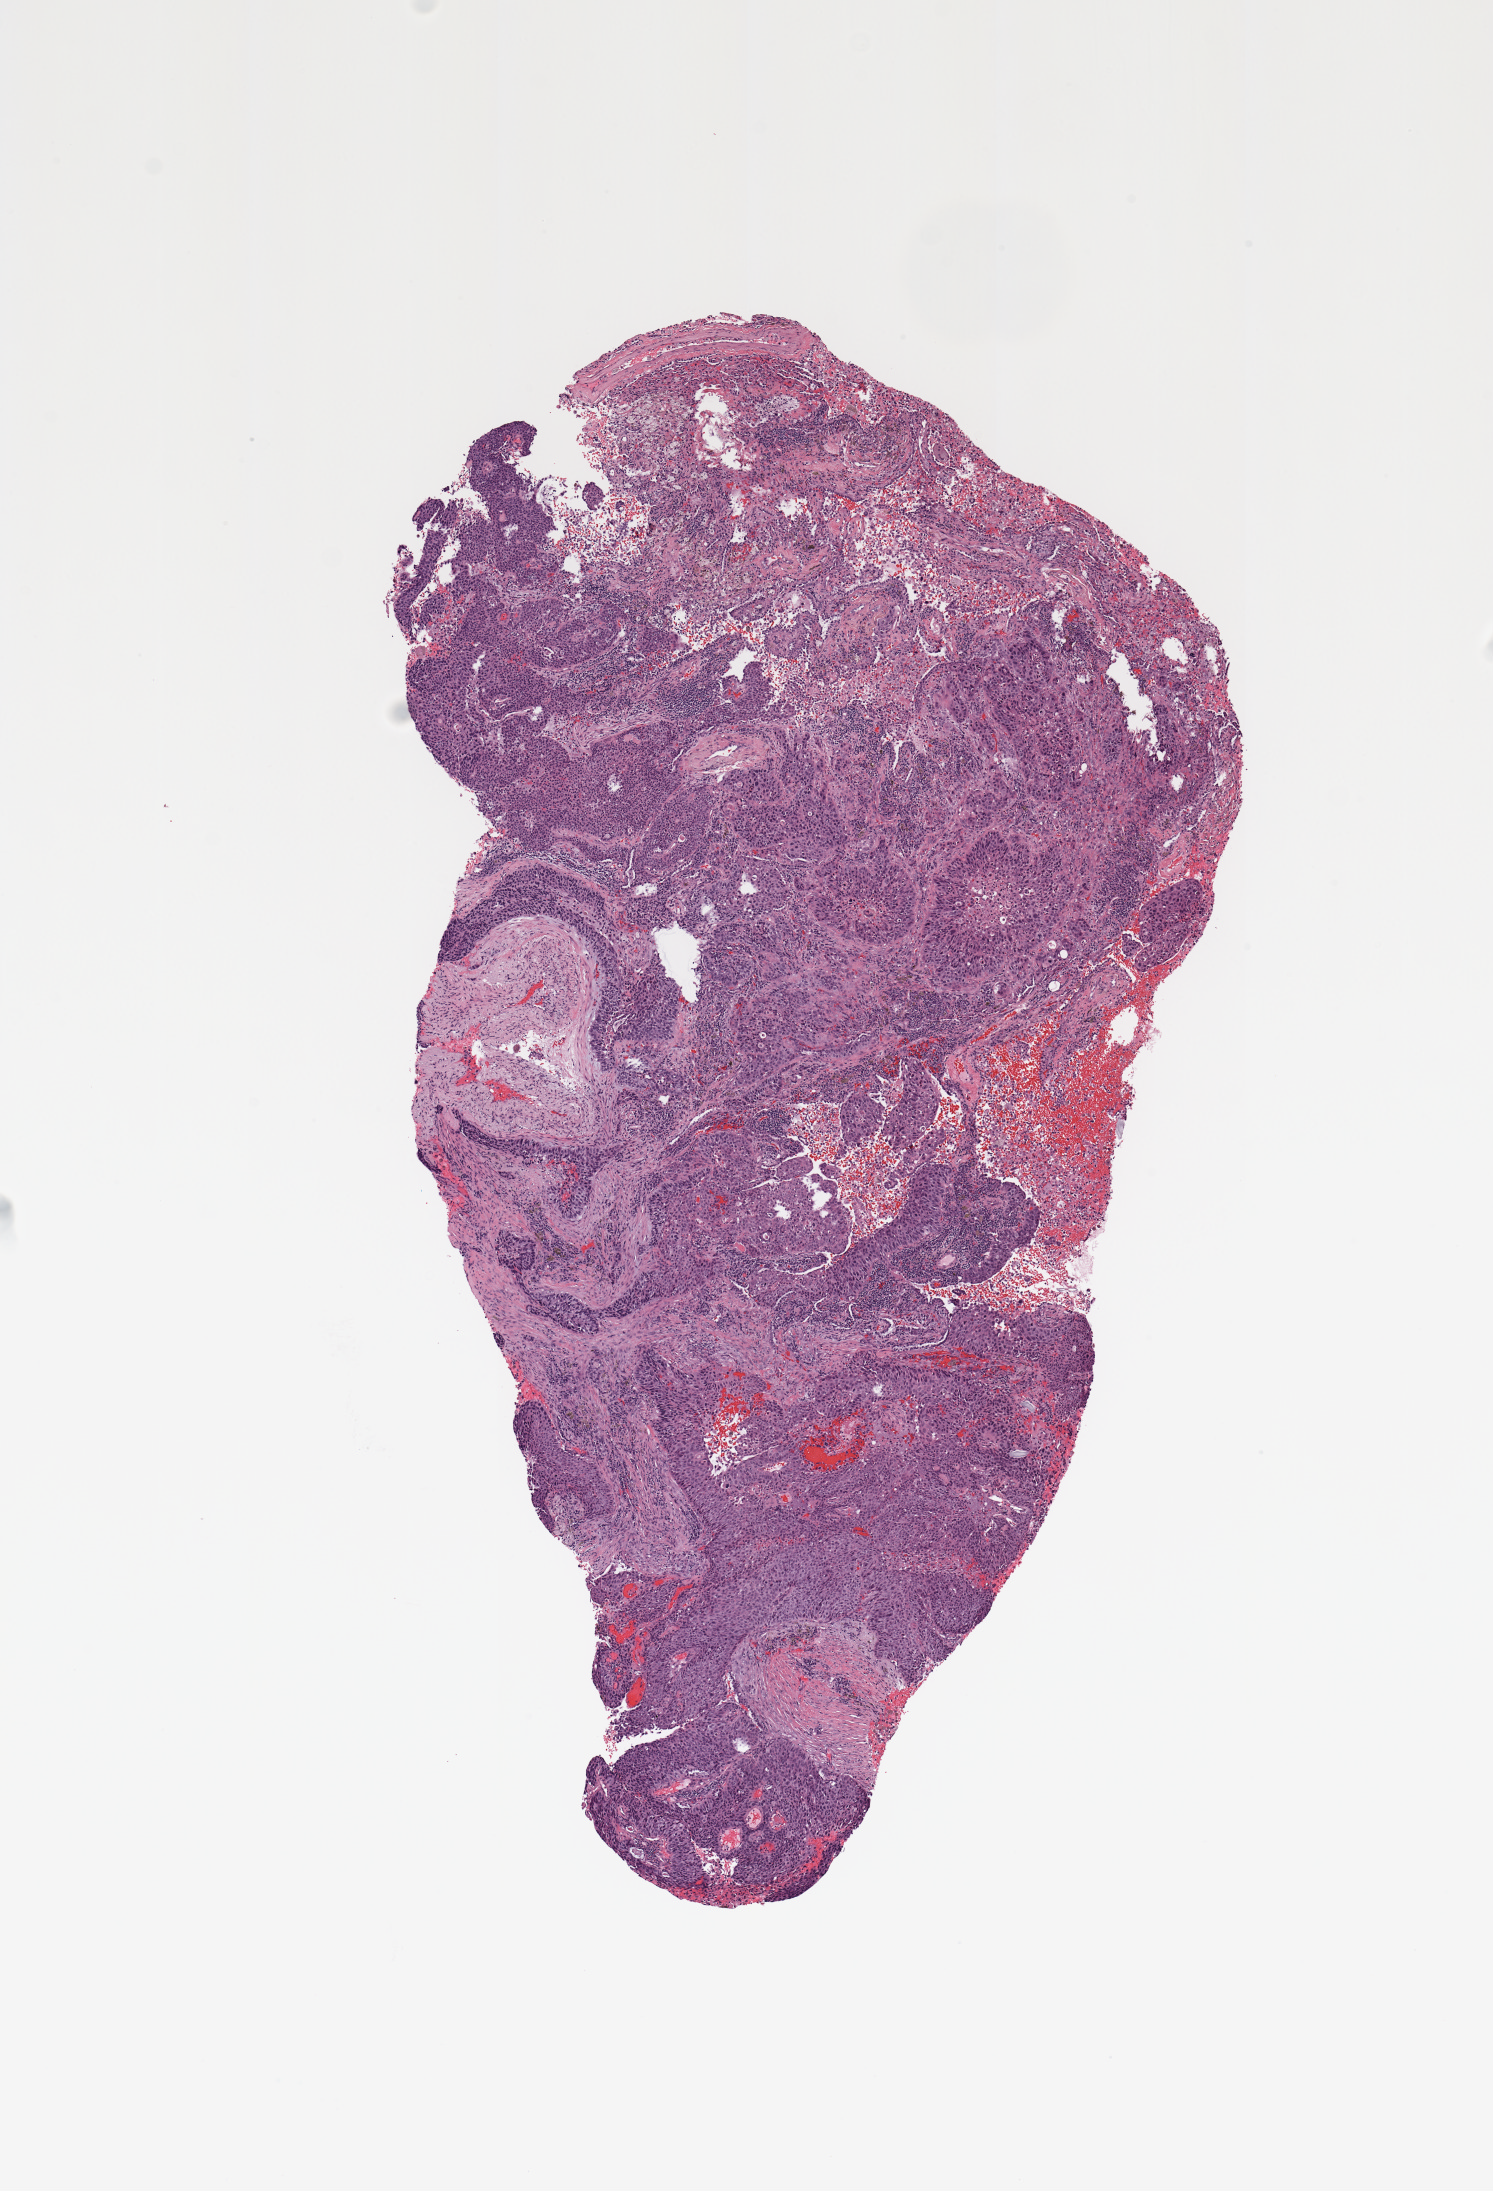
Whole-slide histology image, H&E-stained, low-resolution overview of the scanned area, about 5.9 x 8.7 mm. Tumour tissue sample, lung. Patient: male, age 49 years. Histologic grade: G3 (poorly differentiated).
• AJCC pathologic stage: IIIA
• primary tumour site (as recorded): left lower lobe
• histologic diagnosis: Squamous cell carcinoma, NOS